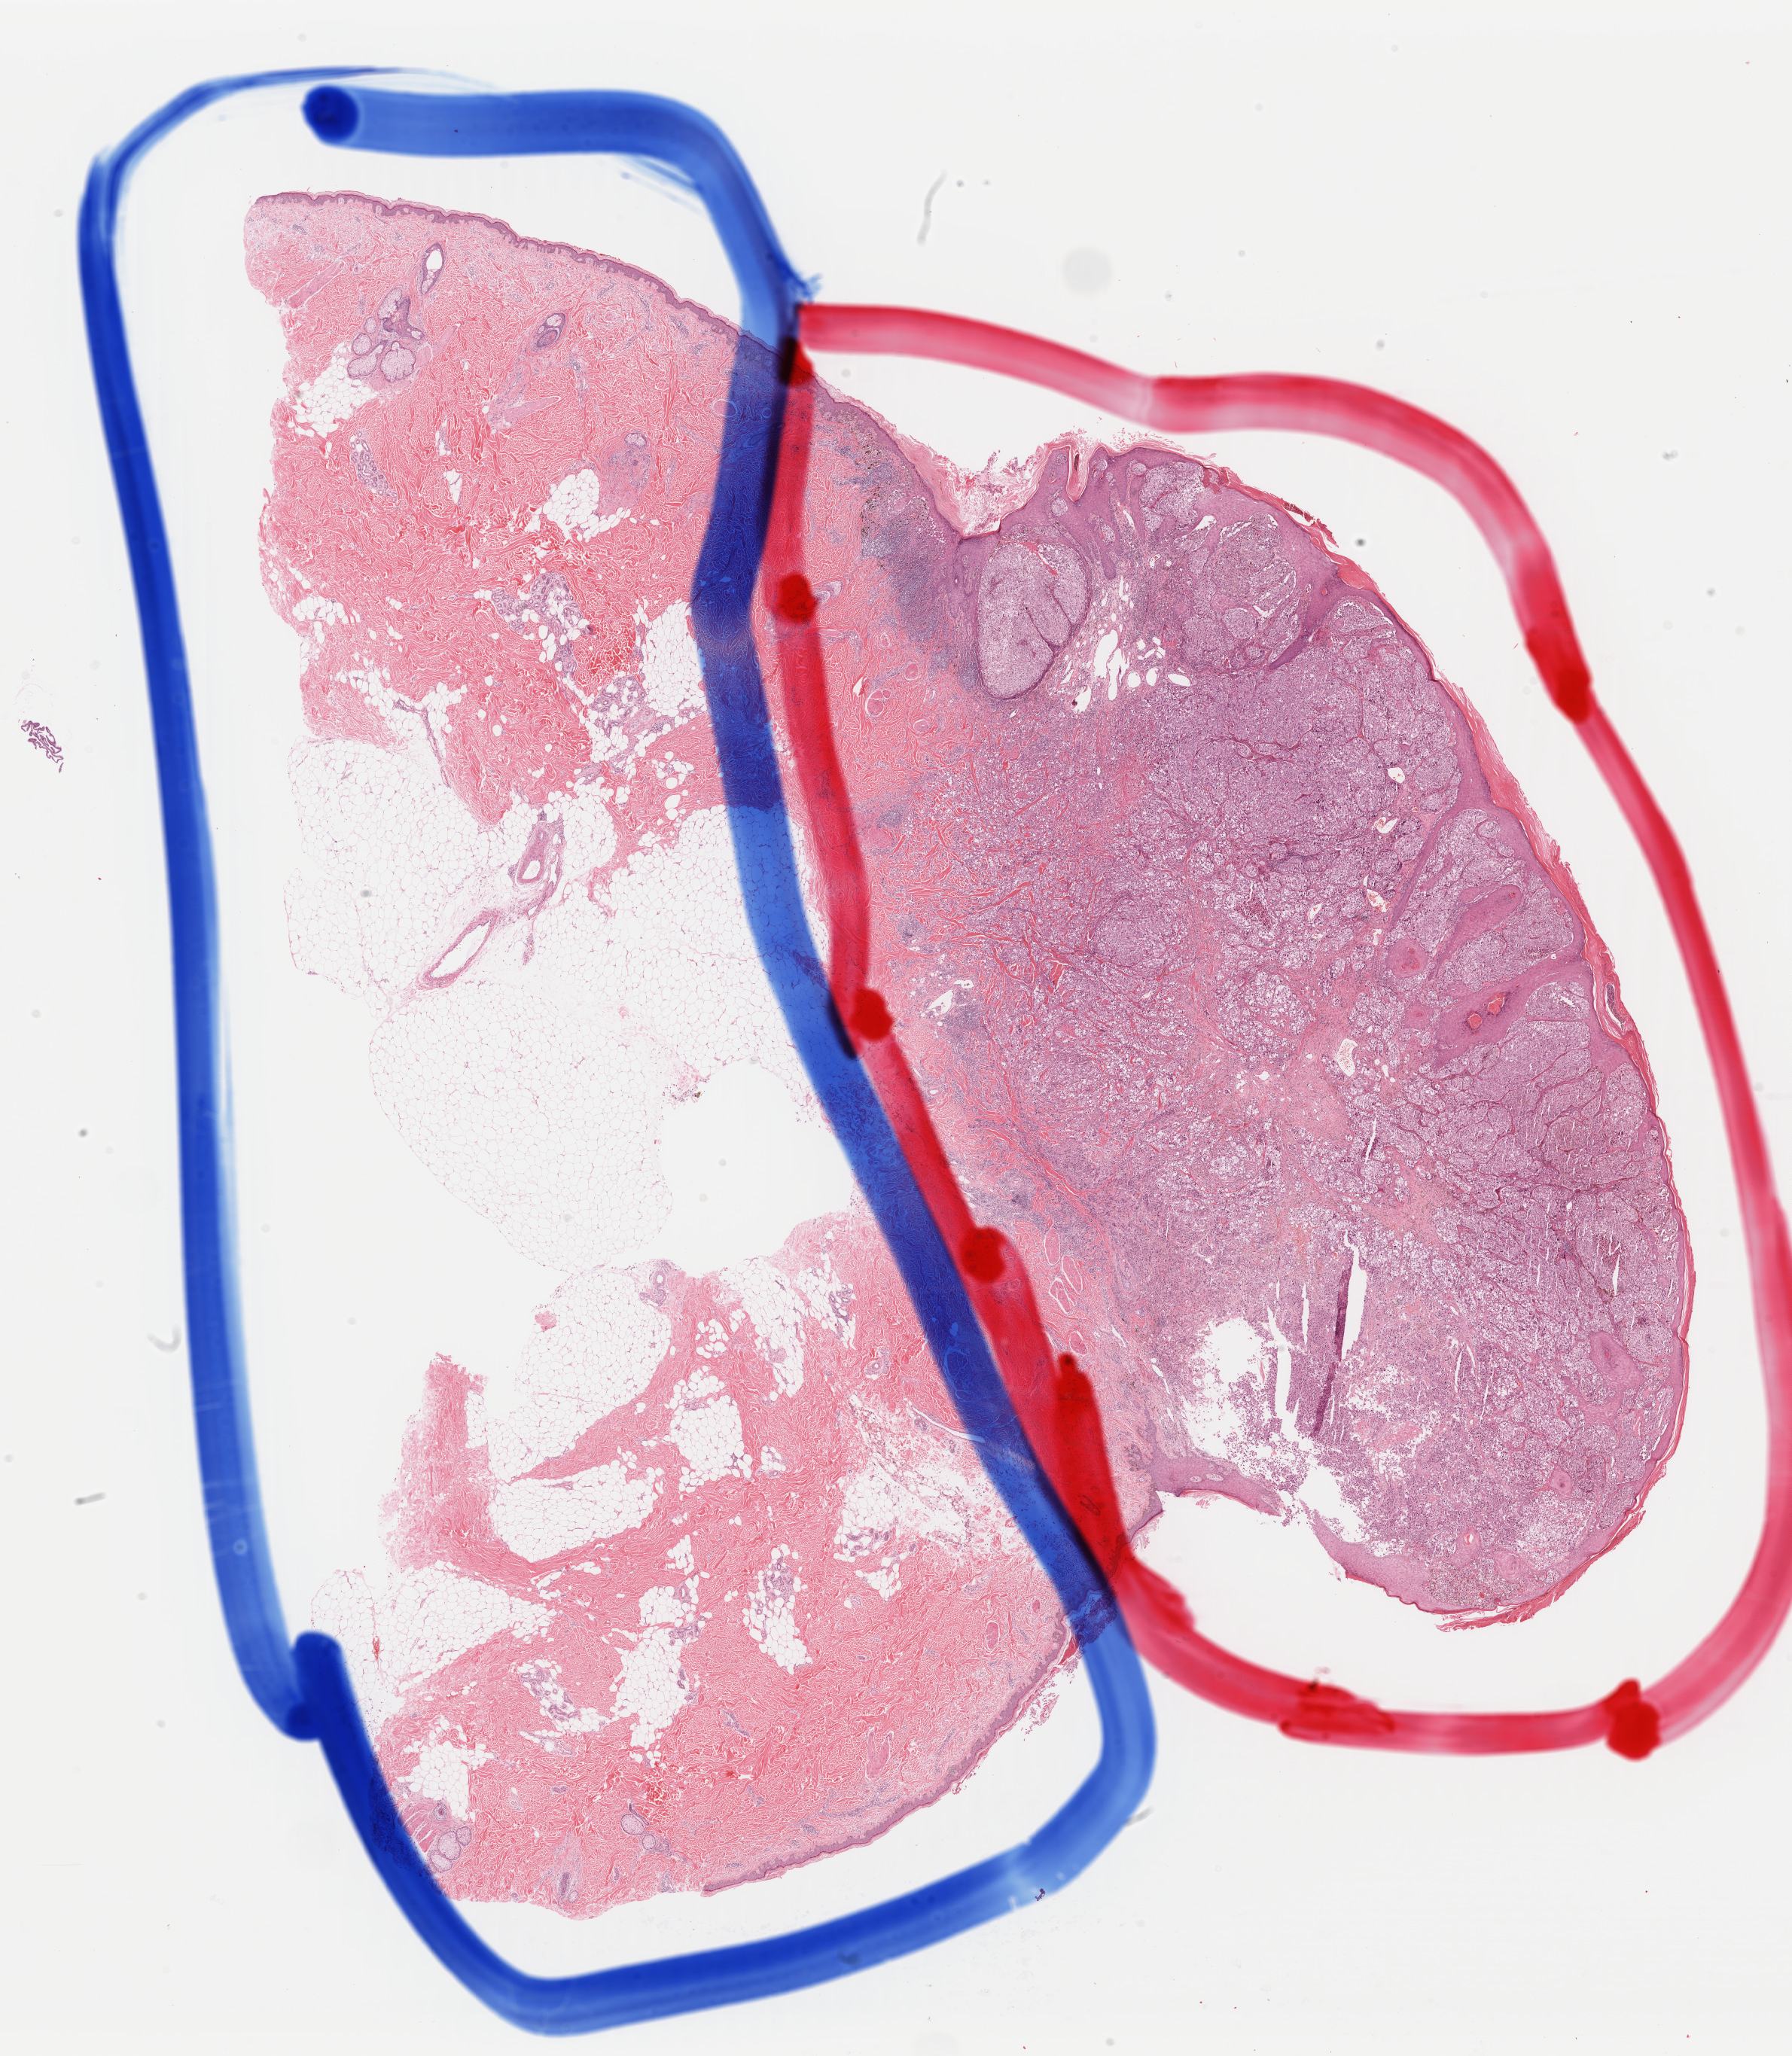
Whole-slide histology image, H&E — whole scanned area (about 18.8 x 21.5 mm) shown as a low-resolution overview; formalin-fixed paraffin-embedded (FFPE) diagnostic section; primary tumour sample from the skin. Male, age 71 years at initial diagnosis.
Pathologic diagnosis: Malignant melanoma, NOS. AJCC pathologic stage: IIC (7th edition).